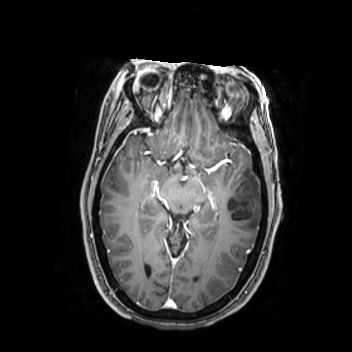
Brain MRI from a brain-tumour surgery series, one axial slice. Position 153 of 350 along the scan axis. T1-weighted post-contrast. 352 × 352 image matrix, field of view 280 × 280 mm. From the clinical record (not read from this slice): histopathology: Oligodendroglioma; WHO grade: 2; IDH mutation: yes; tumour location: Left Middle Temporal Gyrus.
Structures marked on this image (outlined manually by an expert reader):
- tumour: bounding box [x1, y1, x2, y2] px = [224, 173, 262, 233]